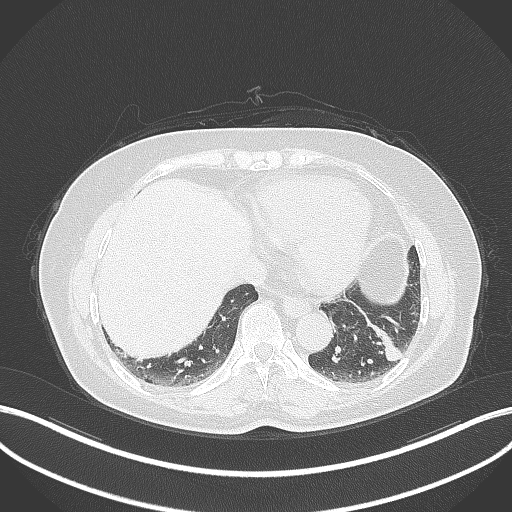
Chest CT, one axial slice; slice 110 of 311 in the series (ordered by position); reconstruction kernel B70f; 120 kVp; lung window (W 1500 / L -600 HU); 1 mm slice thickness; 512 × 512 image matrix, field of view 400 × 400 mm. Patient: female, 59 years. From the clinical record (not read from this slice): clinical TNM (as recorded): T2a N0 M0; histopathological grade: G2-3.
Structures marked on this image (rectangle marked by the reading radiologist):
- lung tumour (recorded histology: adenocarcinoma): bounding box [x1, y1, x2, y2] px = [363, 321, 407, 366]